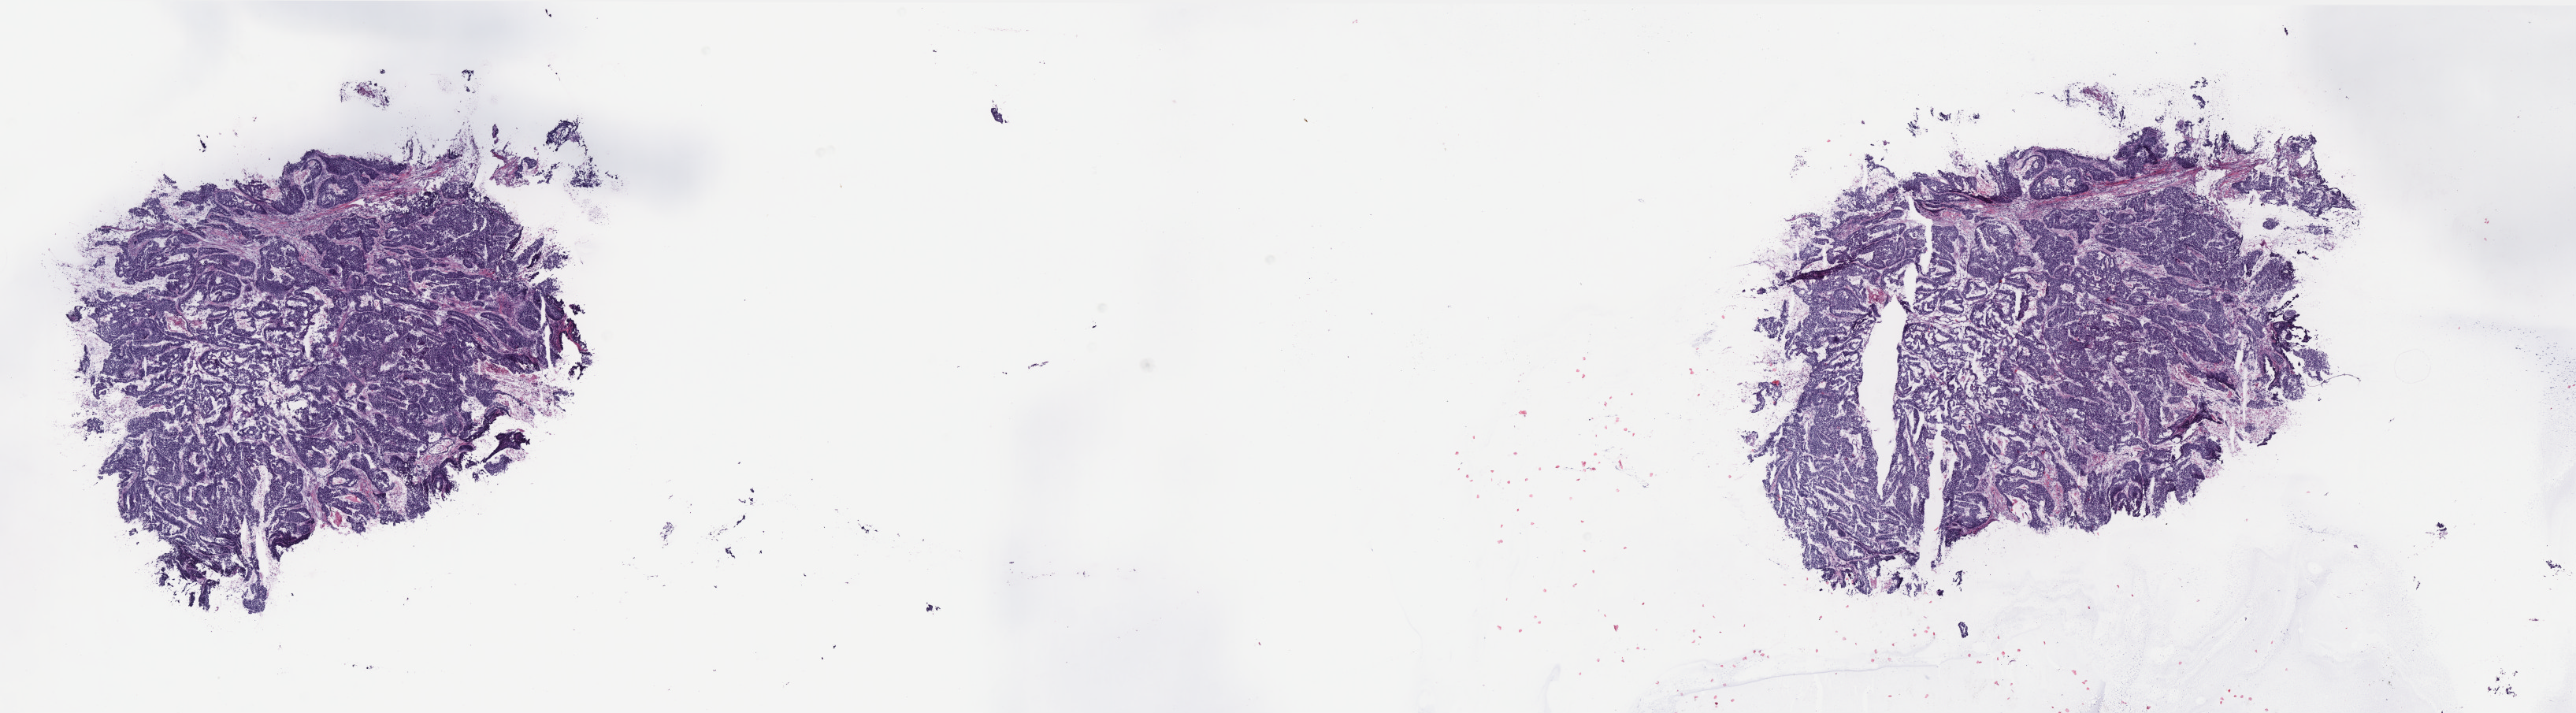
Whole-slide histology image, Hematoxylin and eosin (H&E) stained — whole scanned area (about 26.2 x 7.3 mm, slide scanned at 40x) shown as a low-resolution overview. Frozen section from the top of the tissue portion. Uterus, primary tumour sample. Female, age 60 years at initial diagnosis. Slide review estimates, as recorded: tumour cells 100%, tumour nuclei 85%.
Pathologic diagnosis: Endometrioid adenocarcinoma, NOS.